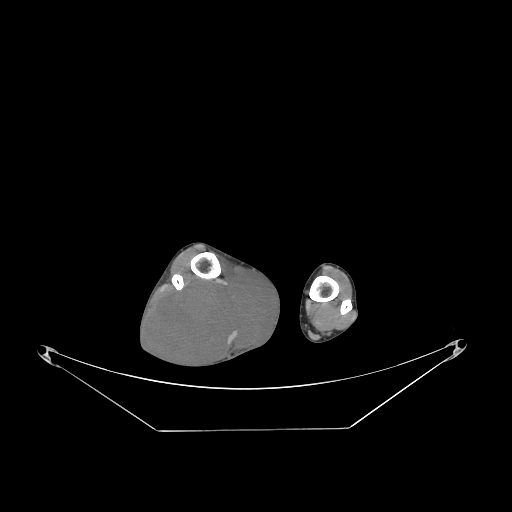
CT of an extremity soft-tissue mass (from a PET/CT study), one axial slice. Position 62 of 267 along the scan axis. Reconstruction kernel STANDARD. 140 kVp. Soft-tissue window (W 400 / L 40 HU). 512 × 512 image matrix, field of view 500 × 500 mm. Male patient. From the clinical record (not read from this slice): histological type: liposarcoma - round cell; grade: high; site of the primary tumour: right calf.
Structures marked on this image (expert contour drawn on MRI and transferred to this co-registered scan by the dataset authors):
- gross tumour volume (mass): bounding box <149,267,279,369> (left, top, right, bottom; pixels)